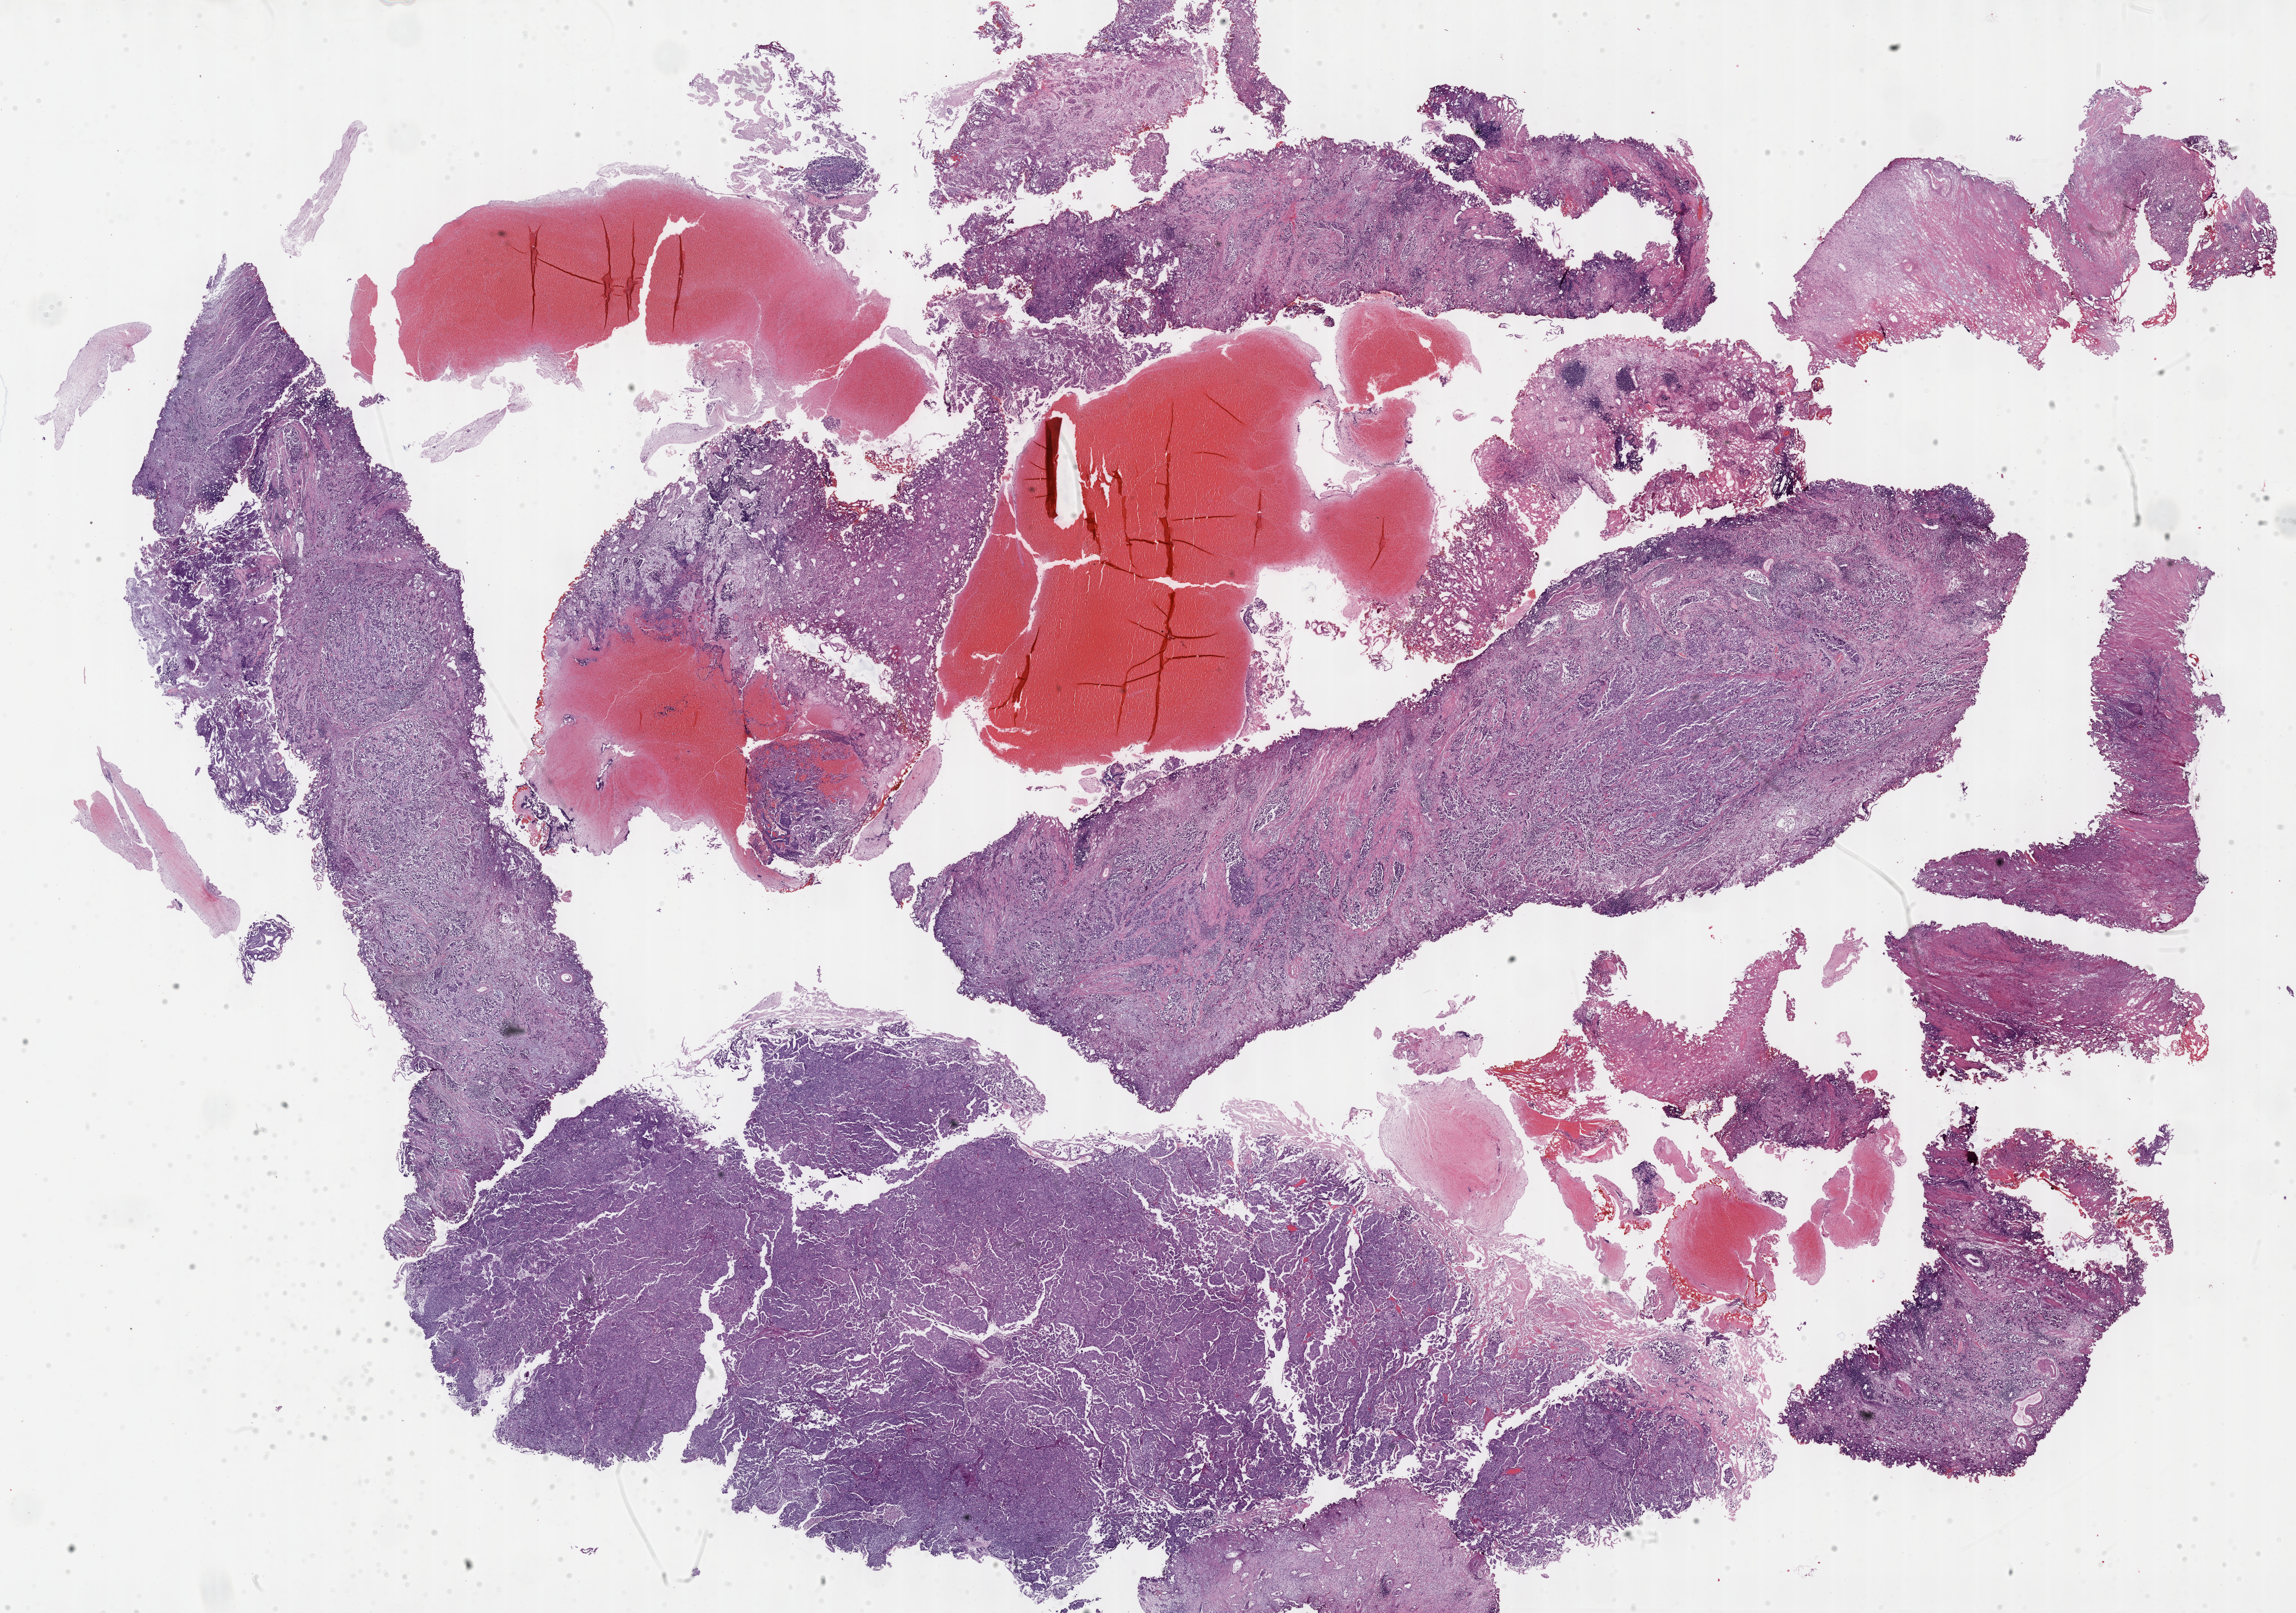
Whole-slide histology image, H&E-stained — low-resolution overview of the scanned area, about 32.2 x 22.6 mm; formalin-fixed paraffin-embedded (FFPE) diagnostic section; primary tumour sample from the bladder. Male patient; age at initial diagnosis 77 years.
Pathologic diagnosis: Transitional cell carcinoma.